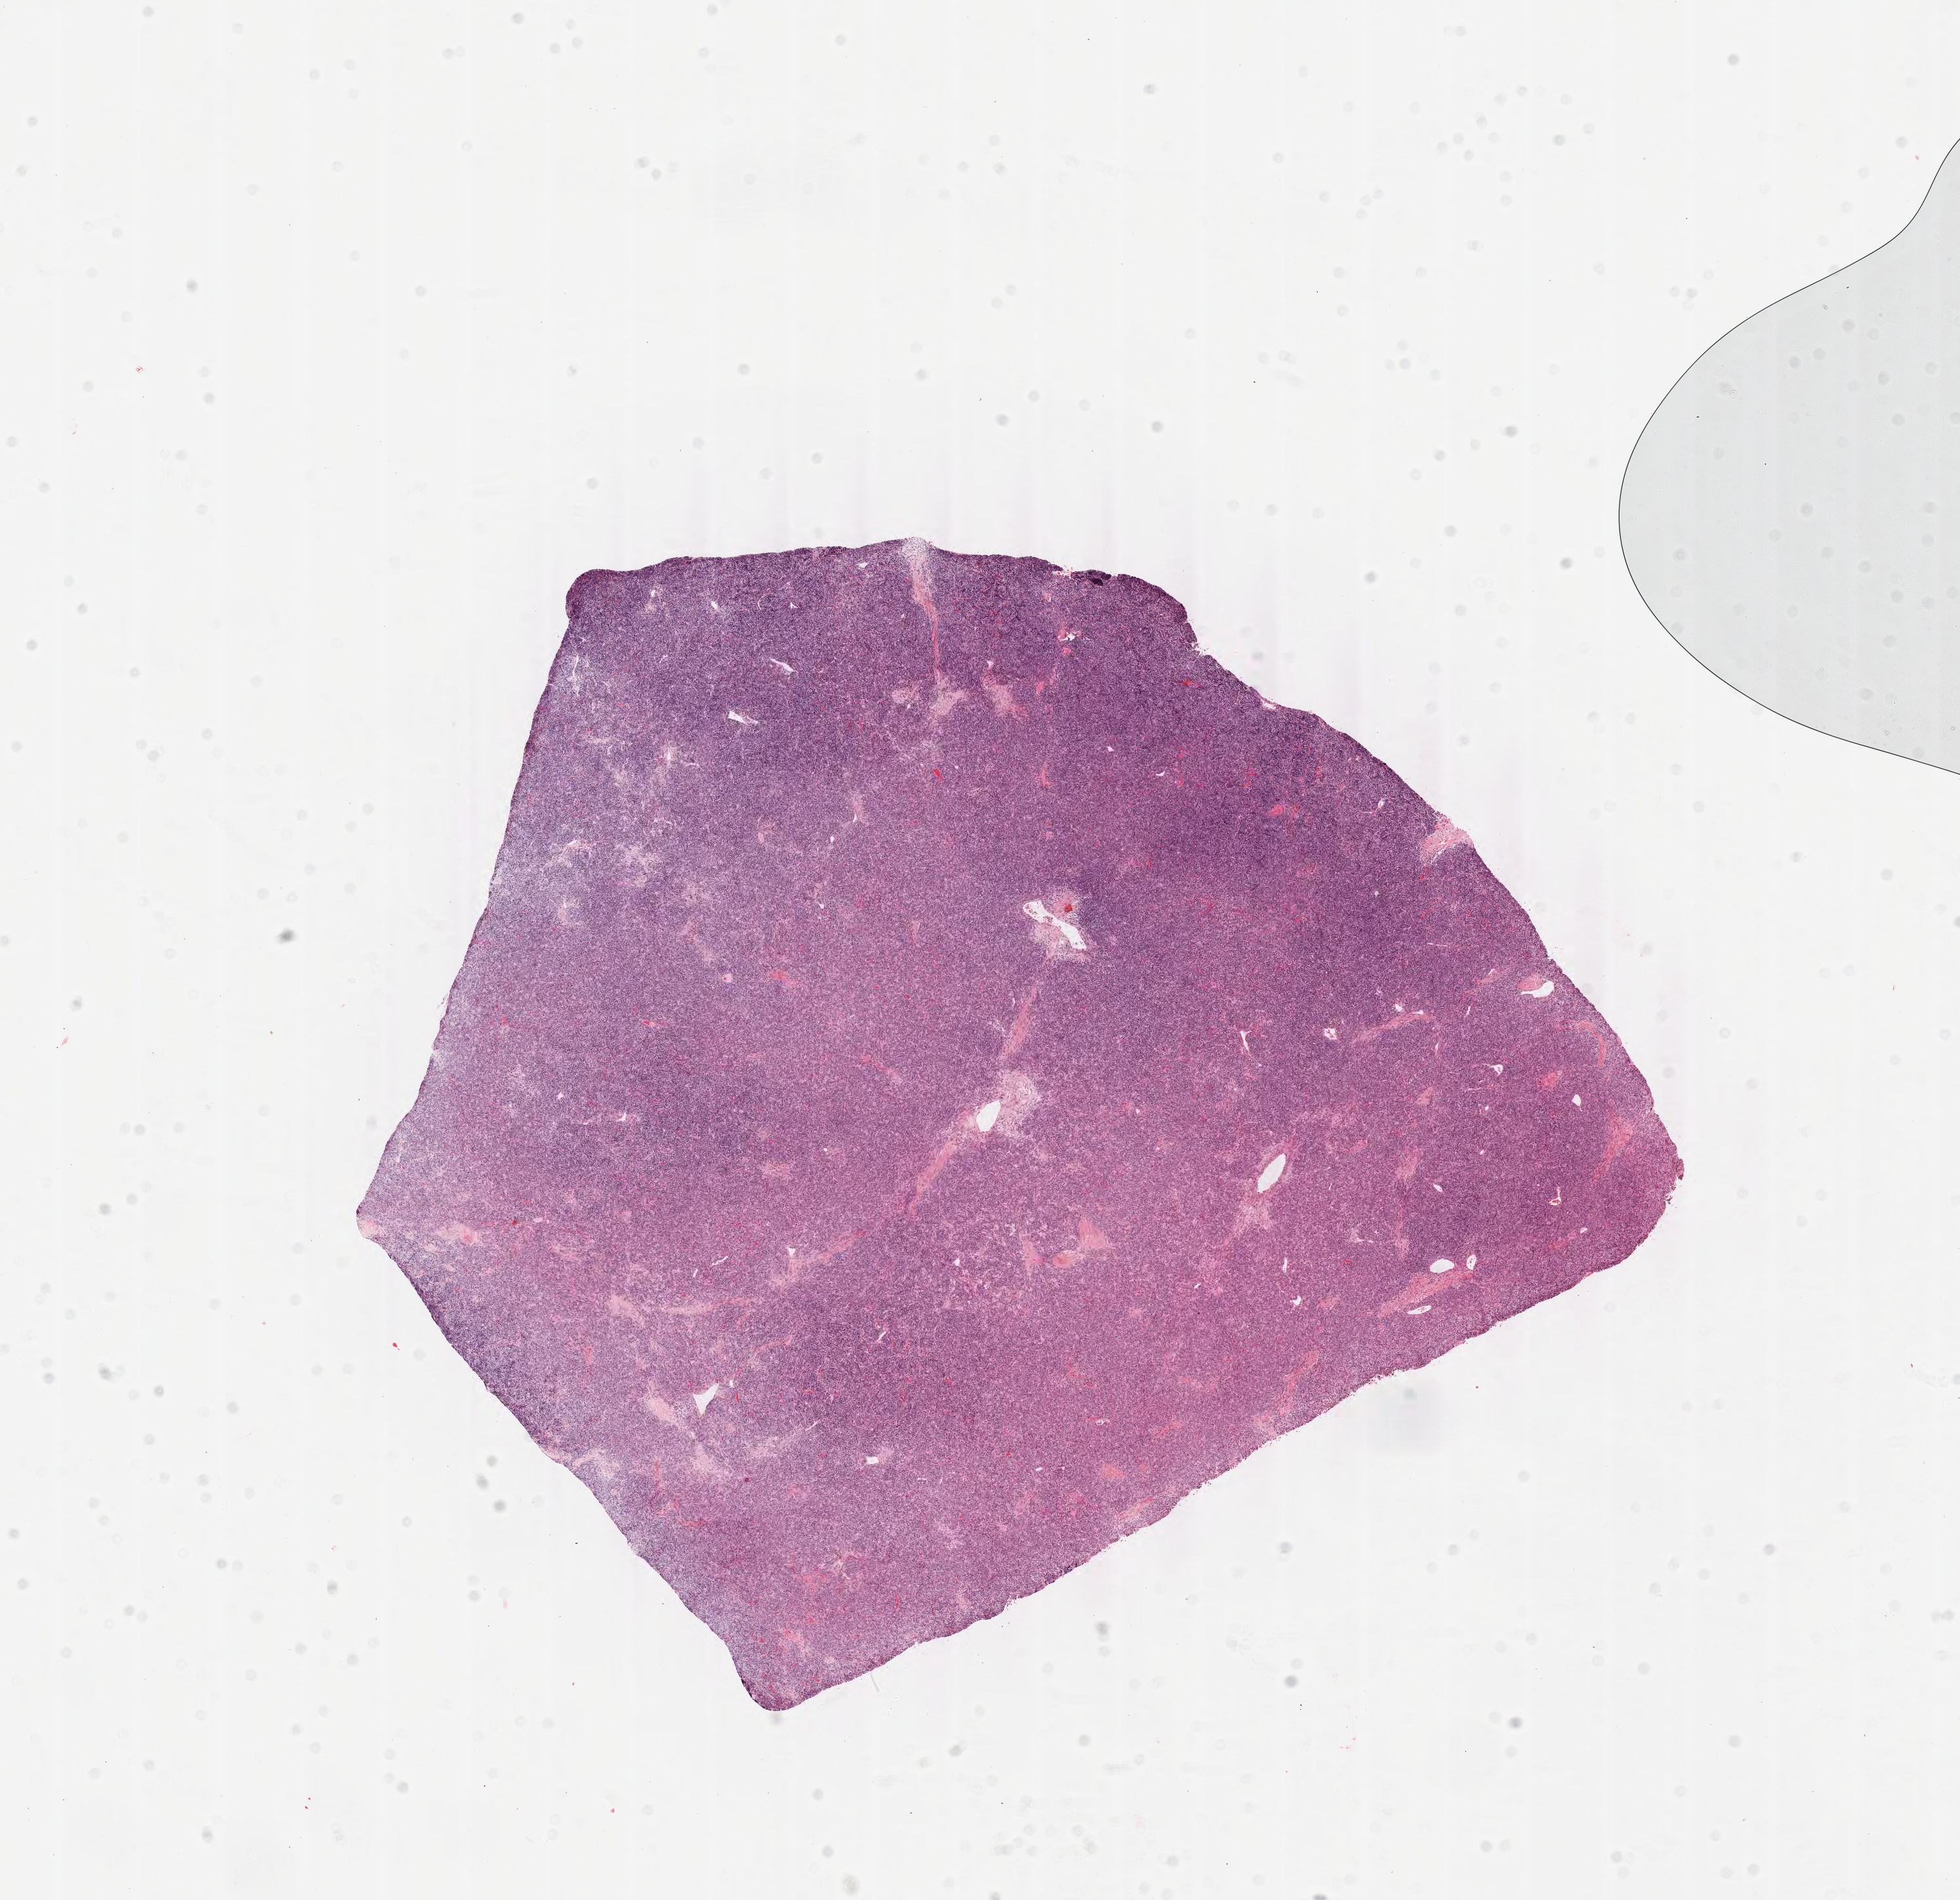
Digitized H&E-stained tissue section (whole slide), a low-resolution overview of the entire scanned area, about 11.8 x 11.4 mm. Formalin-fixed paraffin-embedded (FFPE) diagnostic section. Thymus, primary tumour sample. Male patient; age at initial diagnosis 67 years.
Histologic diagnosis: Thymoma, type B2, malignant.